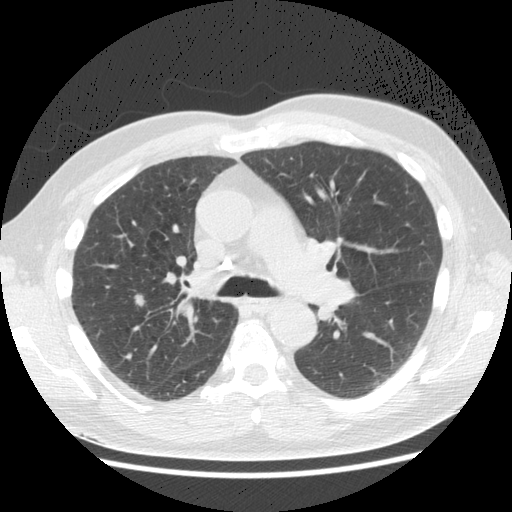
Low-dose screening chest CT, one axial slice; slice 104 of 161 in the series (ordered by position); 120 kVp; lung window (W 1500 / L -600 HU); 512 × 512 image matrix, field of view 360 × 360 mm.
Outlined on this slice (expert manual segmentation):
- lesion 1 (tumor, upper lobe of right lung): box from (x=136, y=295) to (x=145, y=306) px